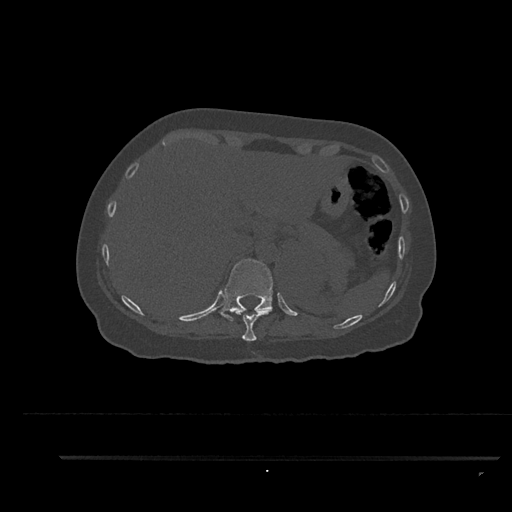
CT including the spine, one axial slice. Position 335 of 797 along the scan axis. Bone window (W 1800 / L 400 HU). 0.5 mm slice thickness. 512 × 512 image matrix, field of view 408 × 408 mm. Female patient, age 44 years. From the clinical record (not read from this slice): primary cancer: renal.
Annotated regions visible in this slice (semi-automatic segmentation, software-assisted and operator-edited):
- T10 vertebra: box from (x=231, y=308) to (x=269, y=341) px
- T11 vertebra: (x=220, y=259)–(x=273, y=322)